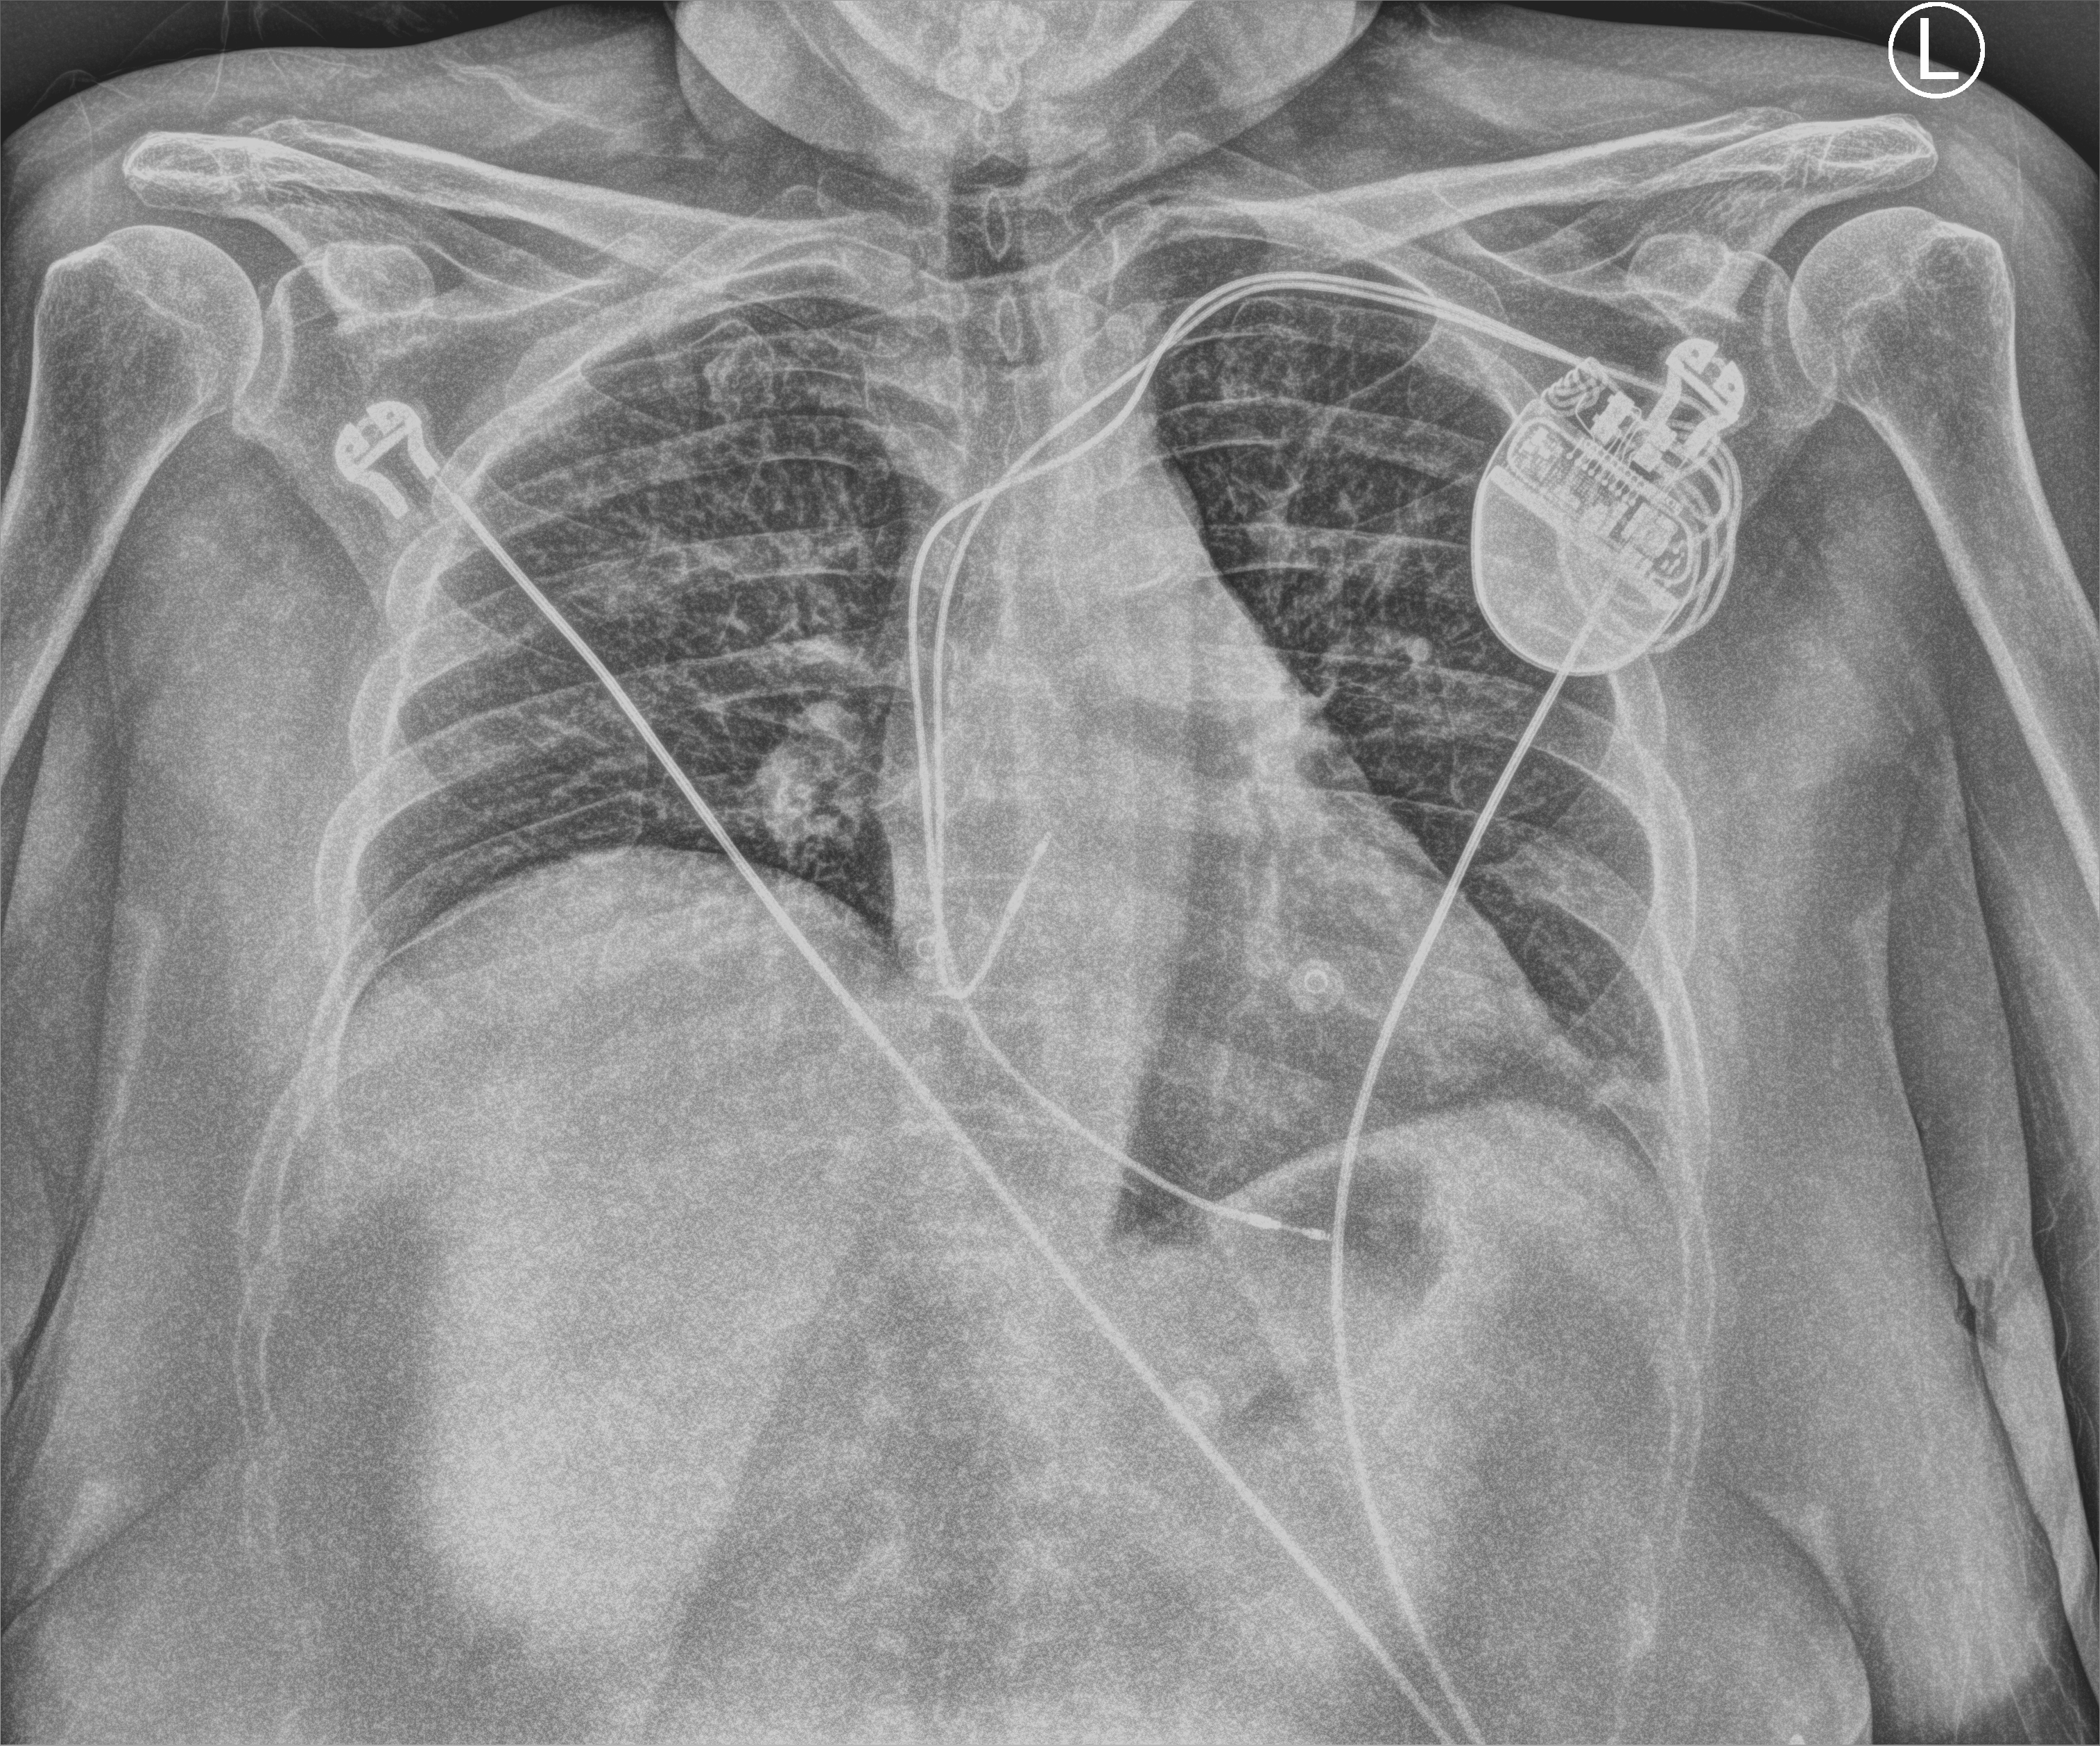
Portable chest radiograph, anteroposterior (AP) projection. Patient hospitalised with COVID-19; female, aged 18–59 years.
From the hospital-stay record, not from the radiograph (when in the stay this image was taken is not recorded): admitted to intensive care during this hospital stay: no.